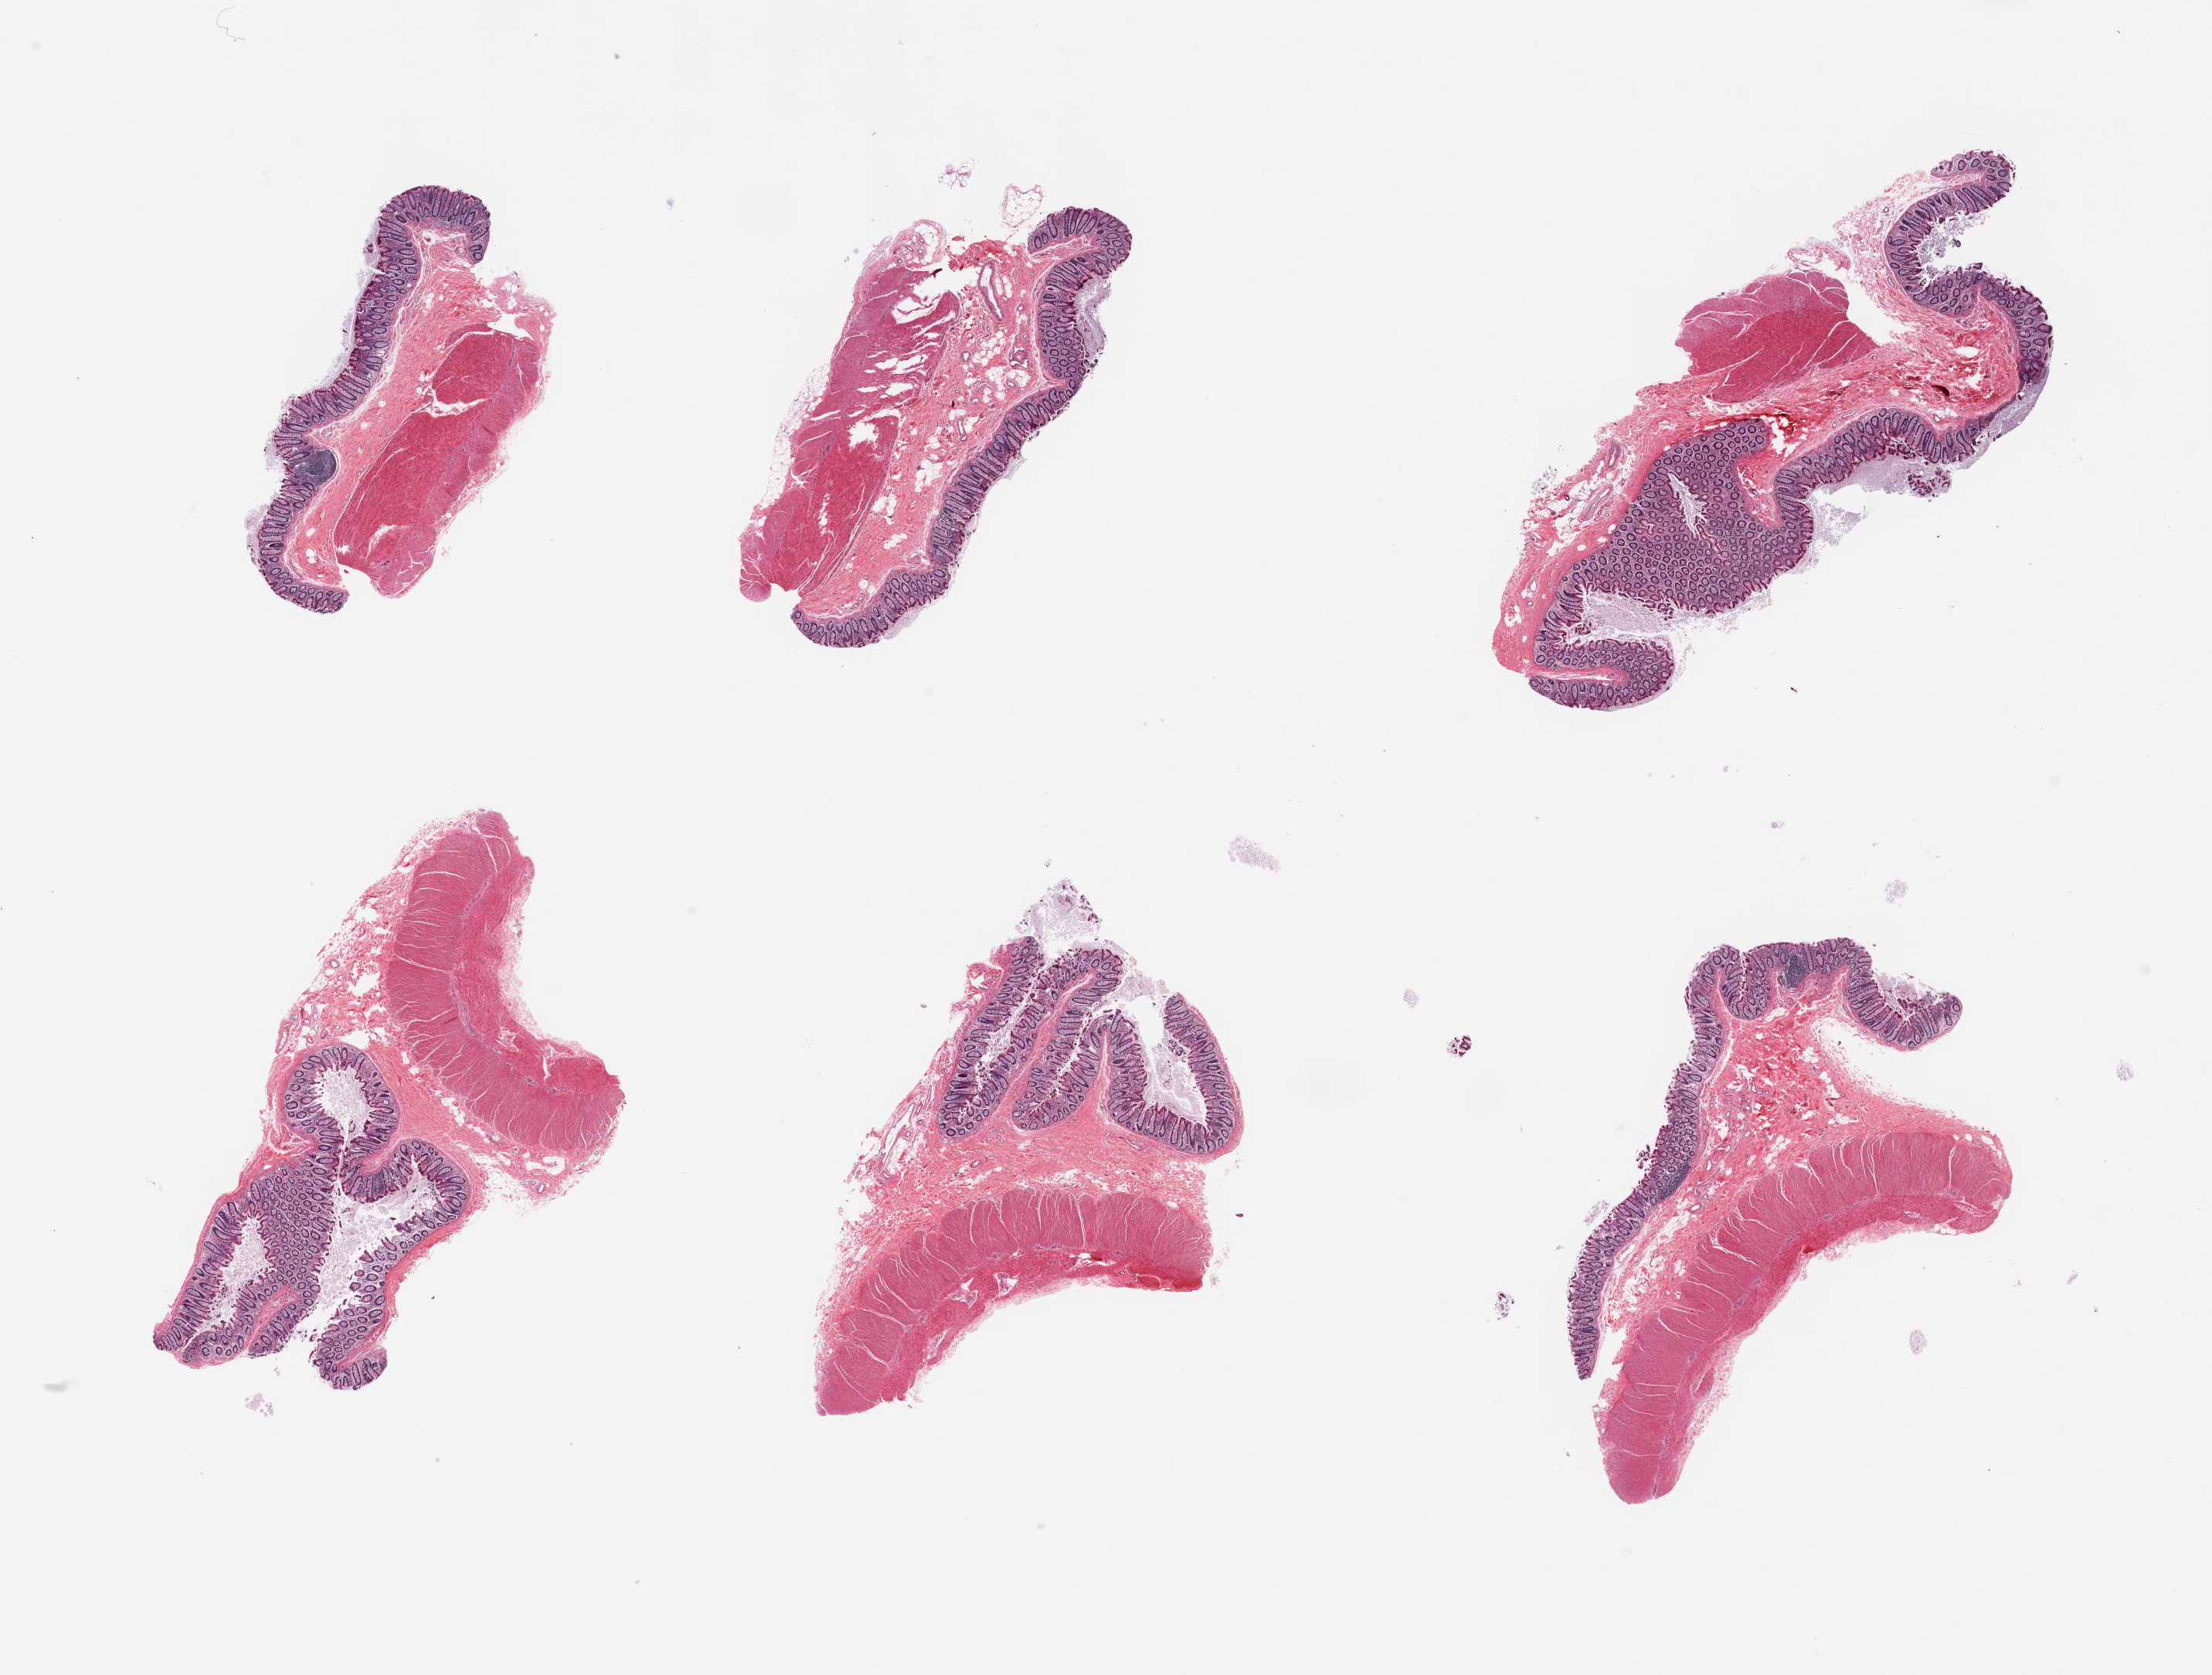
Haematoxylin and eosin whole-slide image, whole scanned area (about 22.6 x 17.1 mm) shown as a low-resolution overview, PAXgene-fixed, paraffin-embedded tissue, section of transverse colon (target tissue), tissue donor sample. Donor sex: male.
Reviewer comment on this tissue sample: 6 pieces, mucosa fairly well preserved, up to ~0.3-0.4mm.